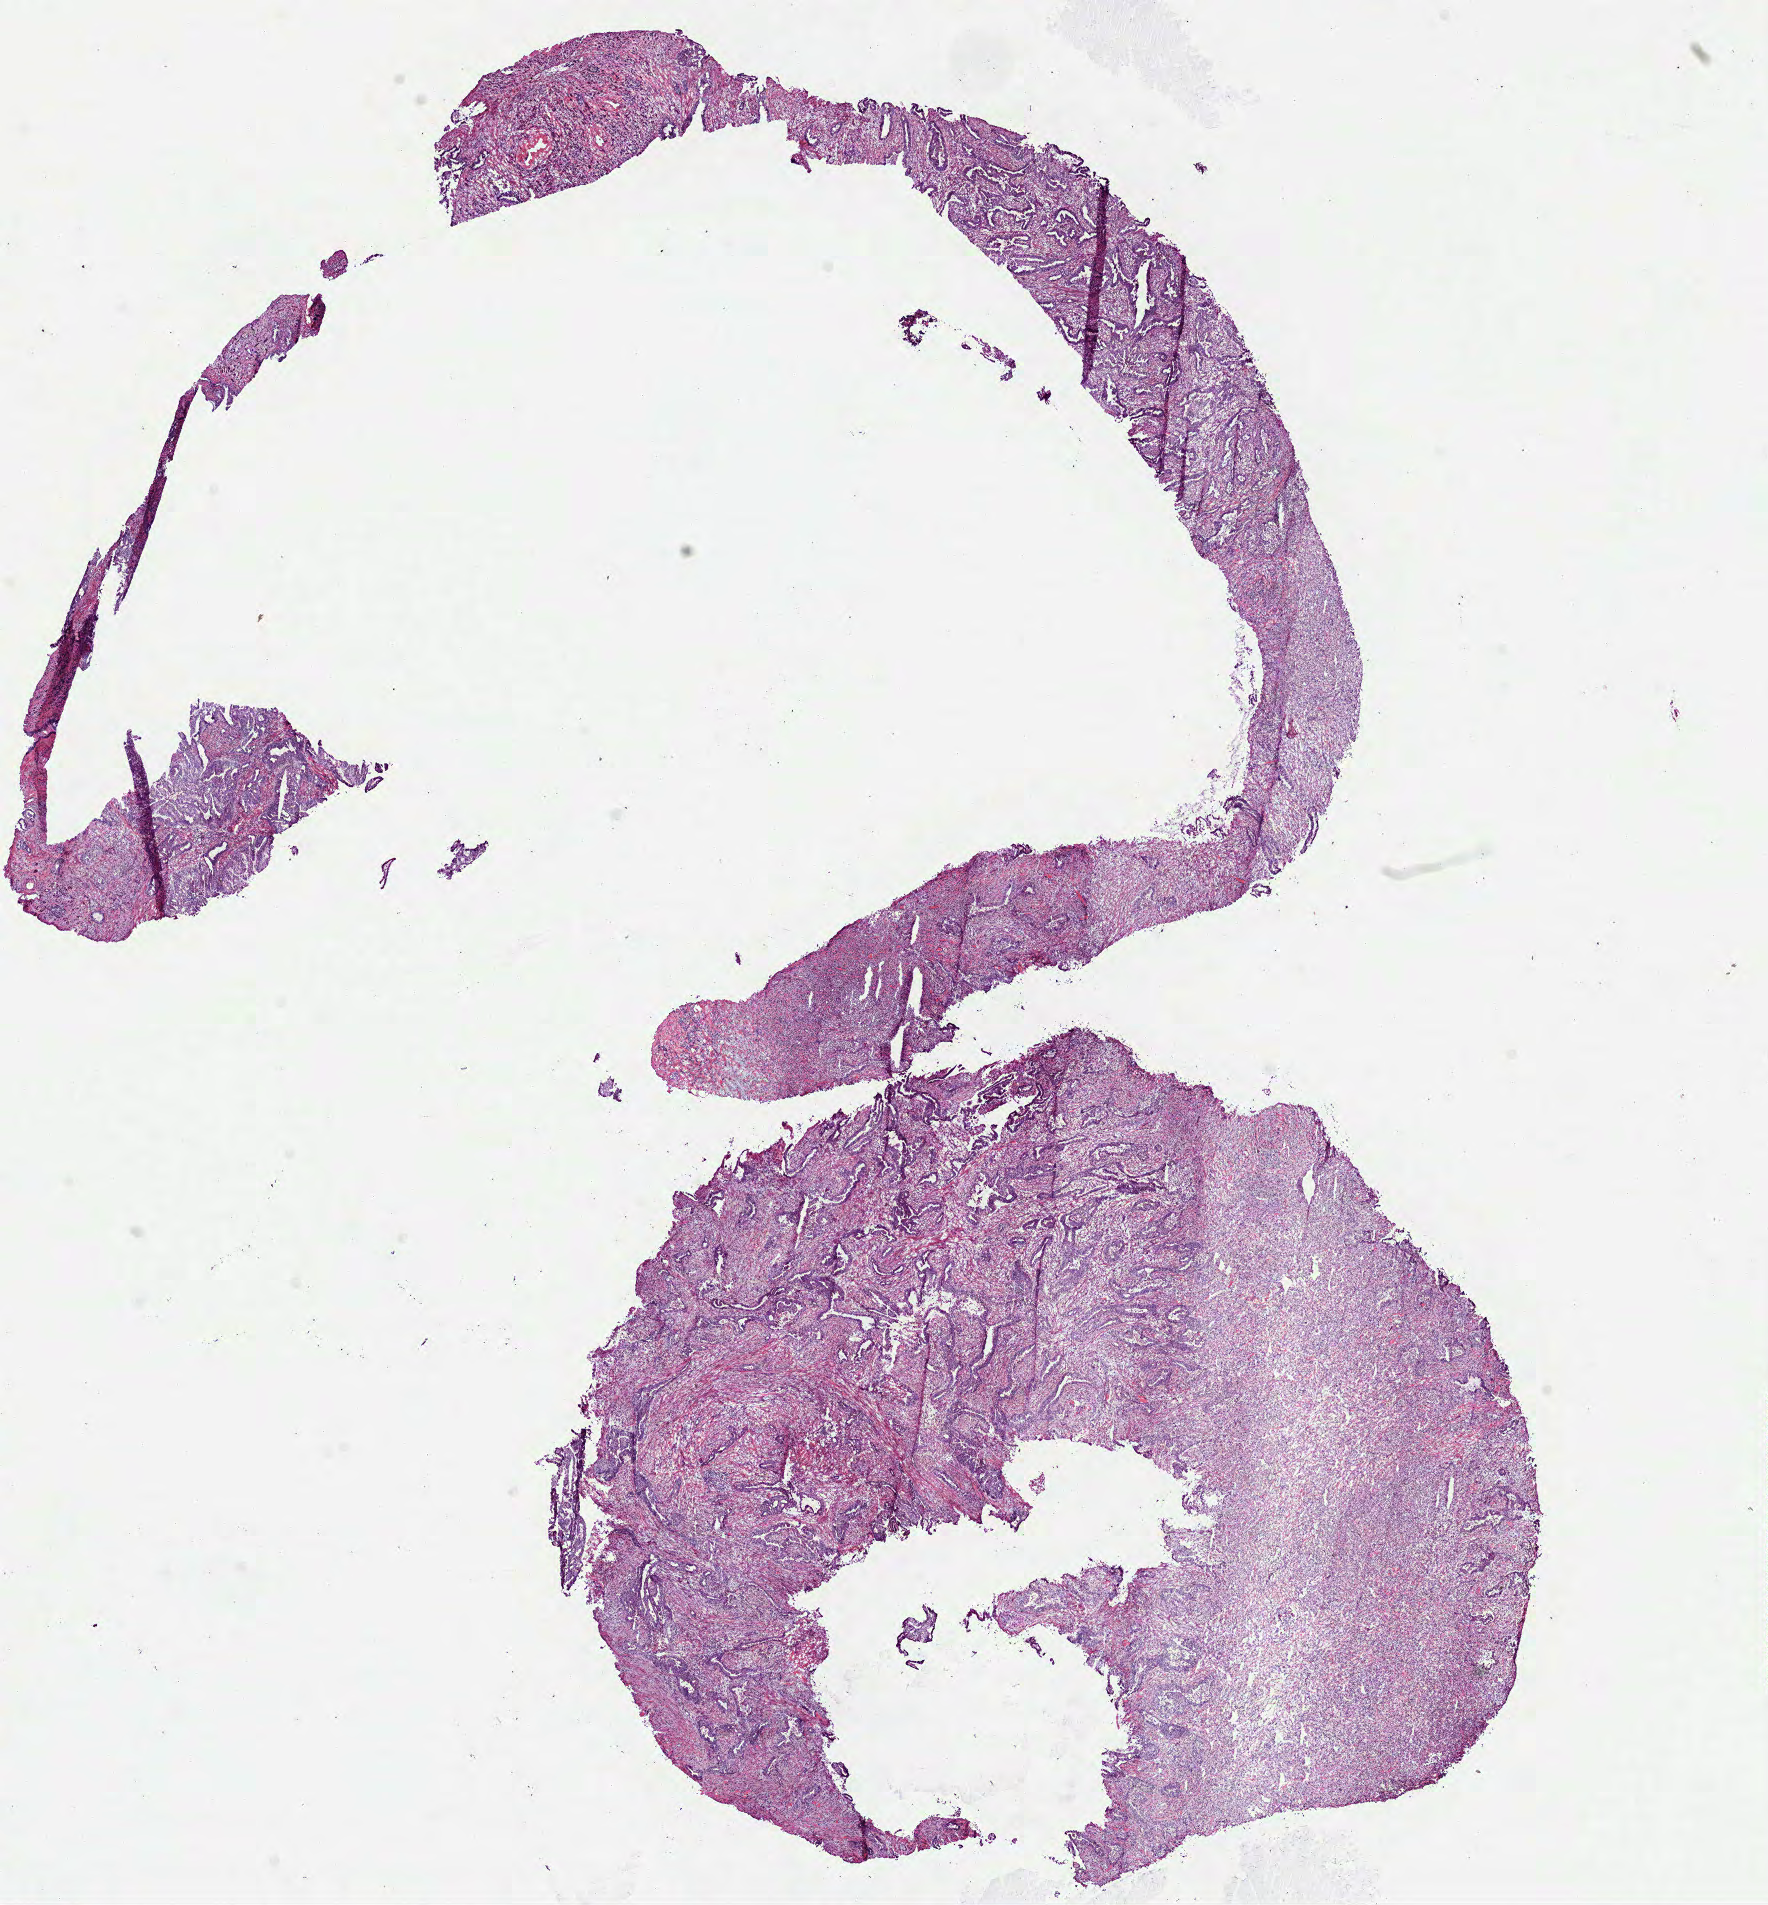
H&E-stained whole-slide image, low-resolution overview of the scanned area, about 14.3 x 15.4 mm (from a 40x scan). Frozen section from the bottom of the tissue portion. Sample: primary tumour, pancreas. Patient: female, age at initial diagnosis 65 years. Histologic grade: G2 (moderately differentiated). Composition of this section per pathologist review: tumour cells 90%, tumour nuclei 50%, normal cells 0%, stromal cells 9%, necrosis 1%. Infiltration values recorded for this section: lymphocyte infiltration 10%, monocyte infiltration 0%, neutrophil infiltration 10%.
AJCC pathologic stage: IV (7th edition). Lymph nodes positive (case pathology): 3 of 8 examined. Pathologic diagnosis: Infiltrating duct carcinoma, NOS (head of pancreas).